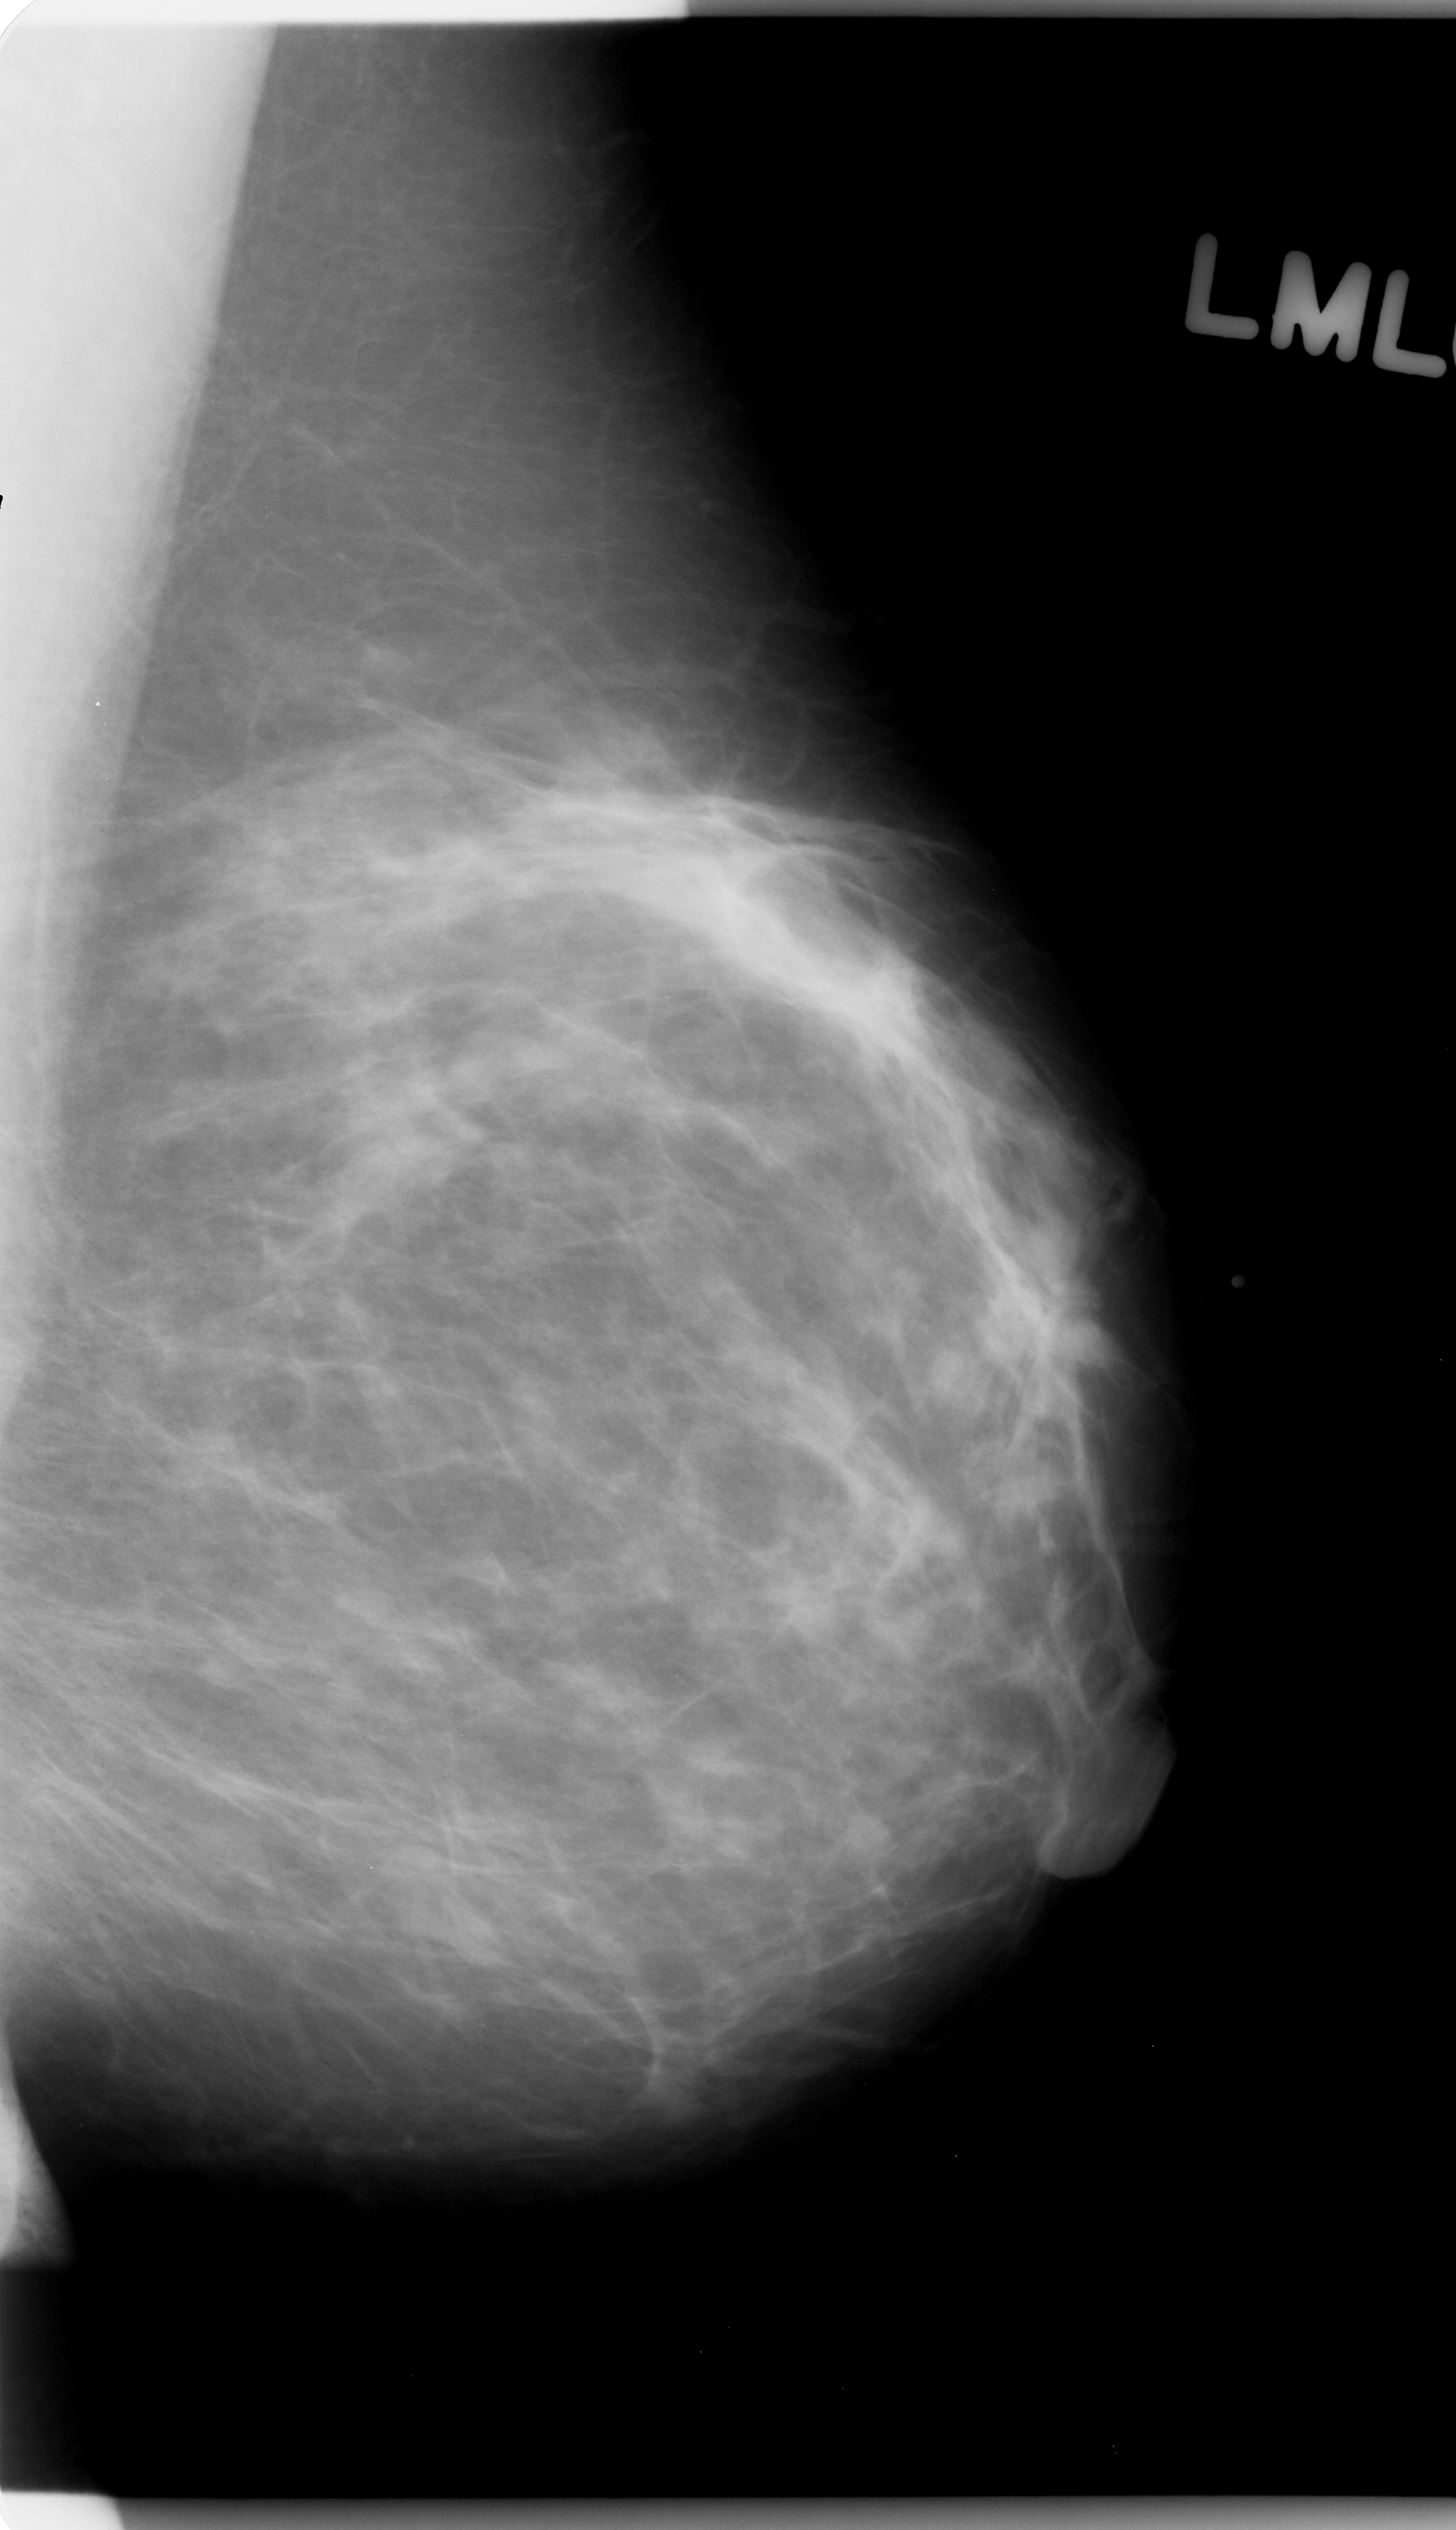
Scanned film-screen mammogram; left breast; mediolateral oblique (MLO) view; BI-RADS breast density category 2 (scale 1–4).
- Mass, shape irregular, margins spiculated; BI-RADS assessment category 5; subtlety rating 4 on a 1 (subtle) to 5 (obvious) scale; pathology result (as recorded, not read from the image): malignant.